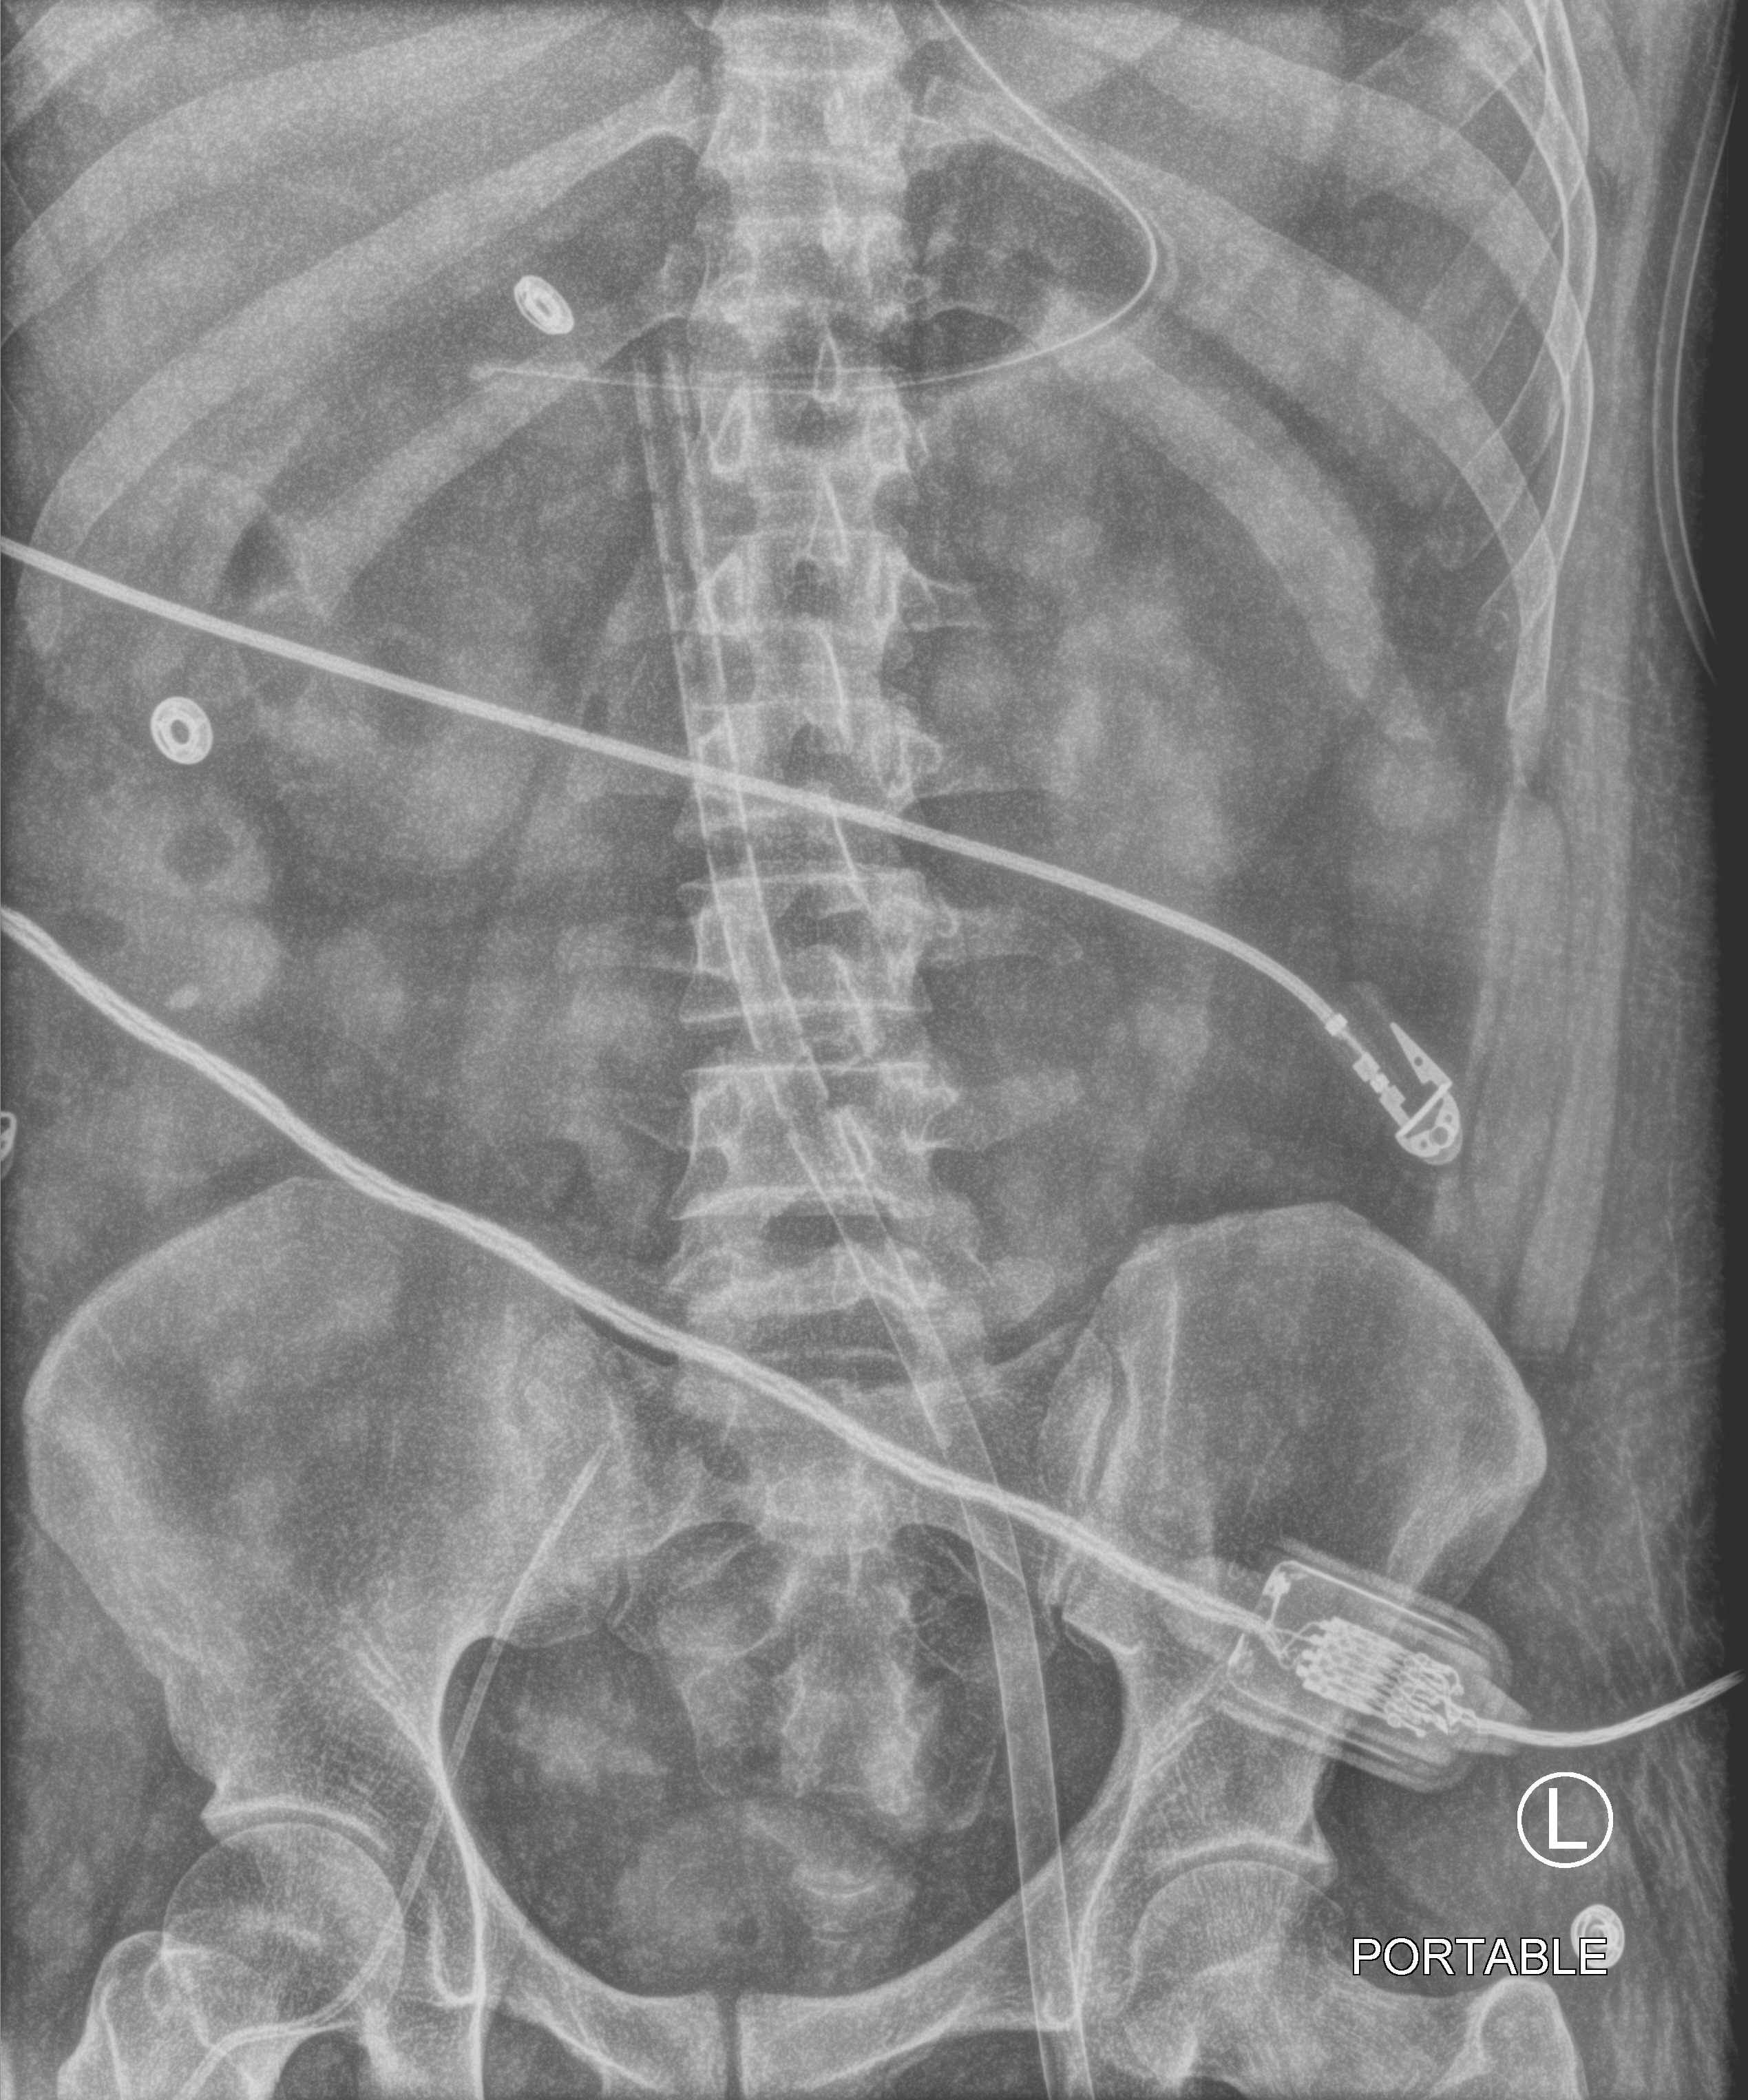
Abdomen X-ray (portable). Adult patient hospitalised with COVID-19, age 18–59 years.
From the hospital-stay record, not from the radiograph (when in the stay this image was taken is not recorded):
- admitted to intensive care during this hospital stay: yes